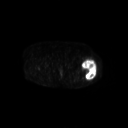
FDG PET of an extremity soft-tissue mass (from a PET/CT study), one axial slice; position 244 of 267 along the scan axis; 3.27 mm slice thickness; 128 × 128 image matrix, field of view 700 × 700 mm. Patient: female, 62 years. Case-level facts recorded for this patient, not image findings: histological type: undifferentiated – high grade; grade: high; site of the primary tumour: left thigh.
Structures marked on this image (expert contour drawn on MRI and transferred to this co-registered scan by the dataset authors):
- gross tumour volume including surrounding oedema: bounding box (x1, y1, x2, y2) in pixels: (81, 59, 97, 81)
- gross tumour volume (mass): (81, 60, 97, 81)